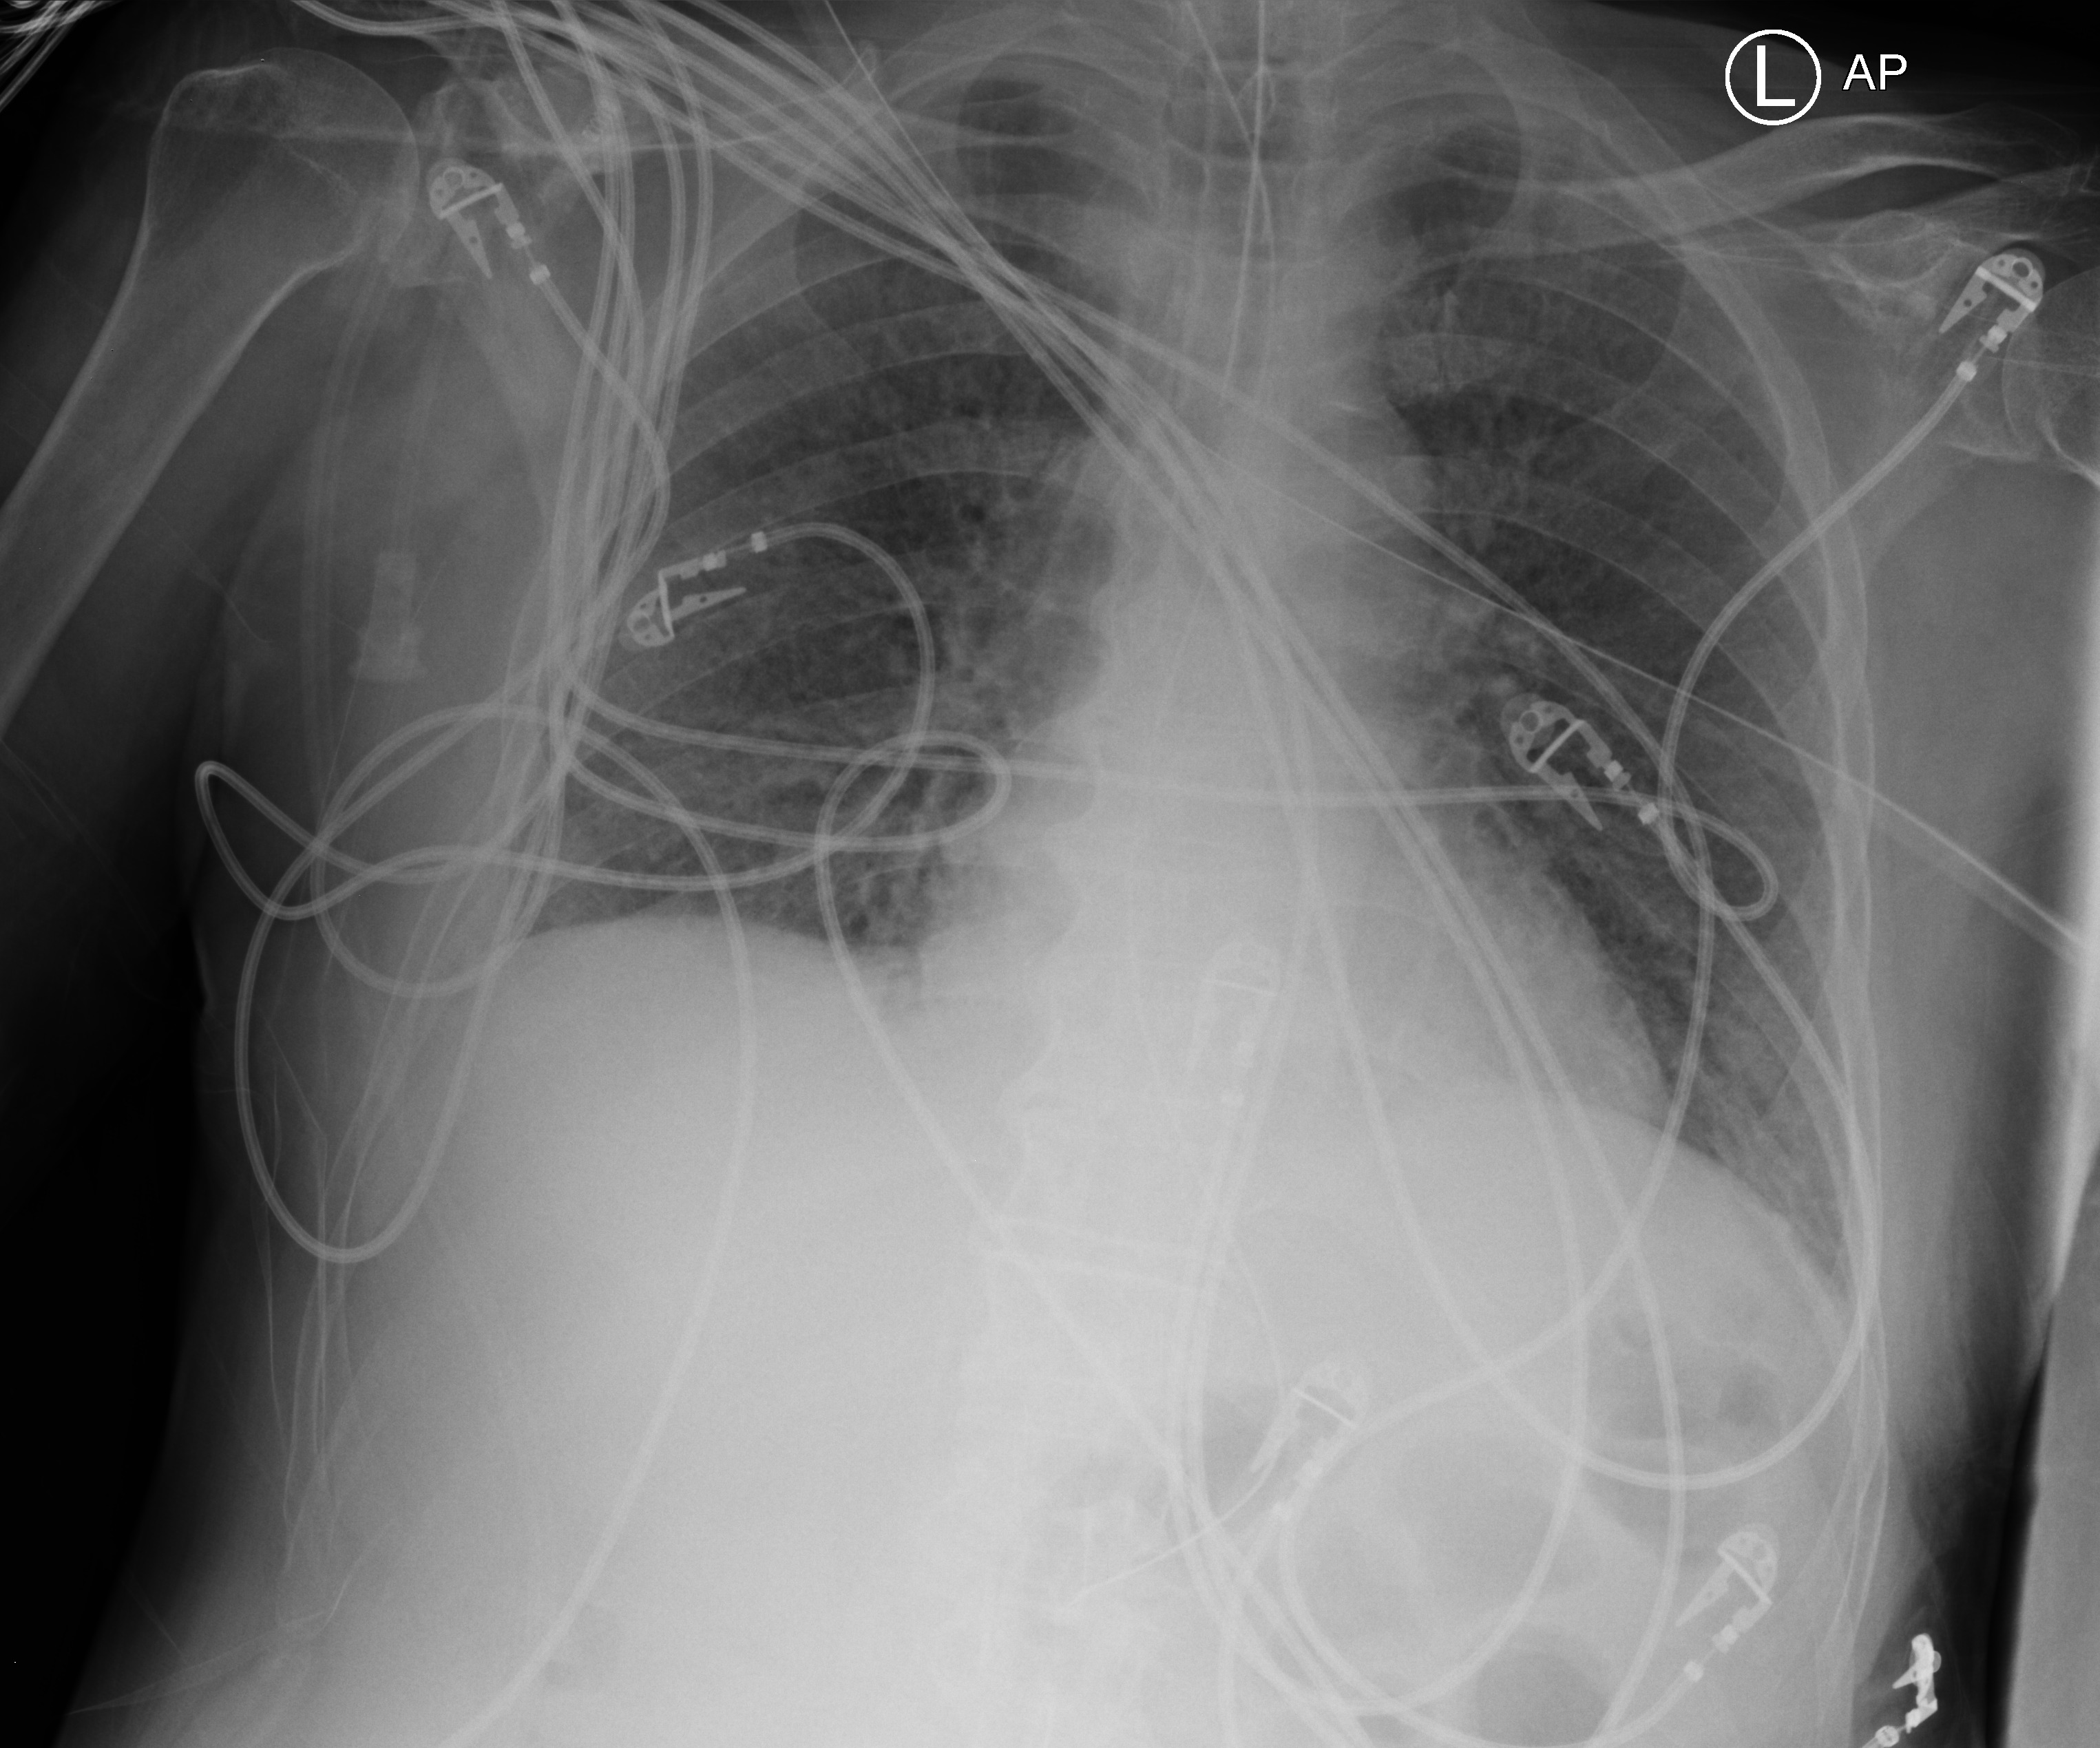
Portable chest radiograph. Male patient hospitalised with COVID-19, age 75–90 years.
From the hospital-stay record, not from the radiograph (when in the stay this image was taken is not recorded): mechanically ventilated during this hospital stay: yes; other chronic lung disease (admission record): no.